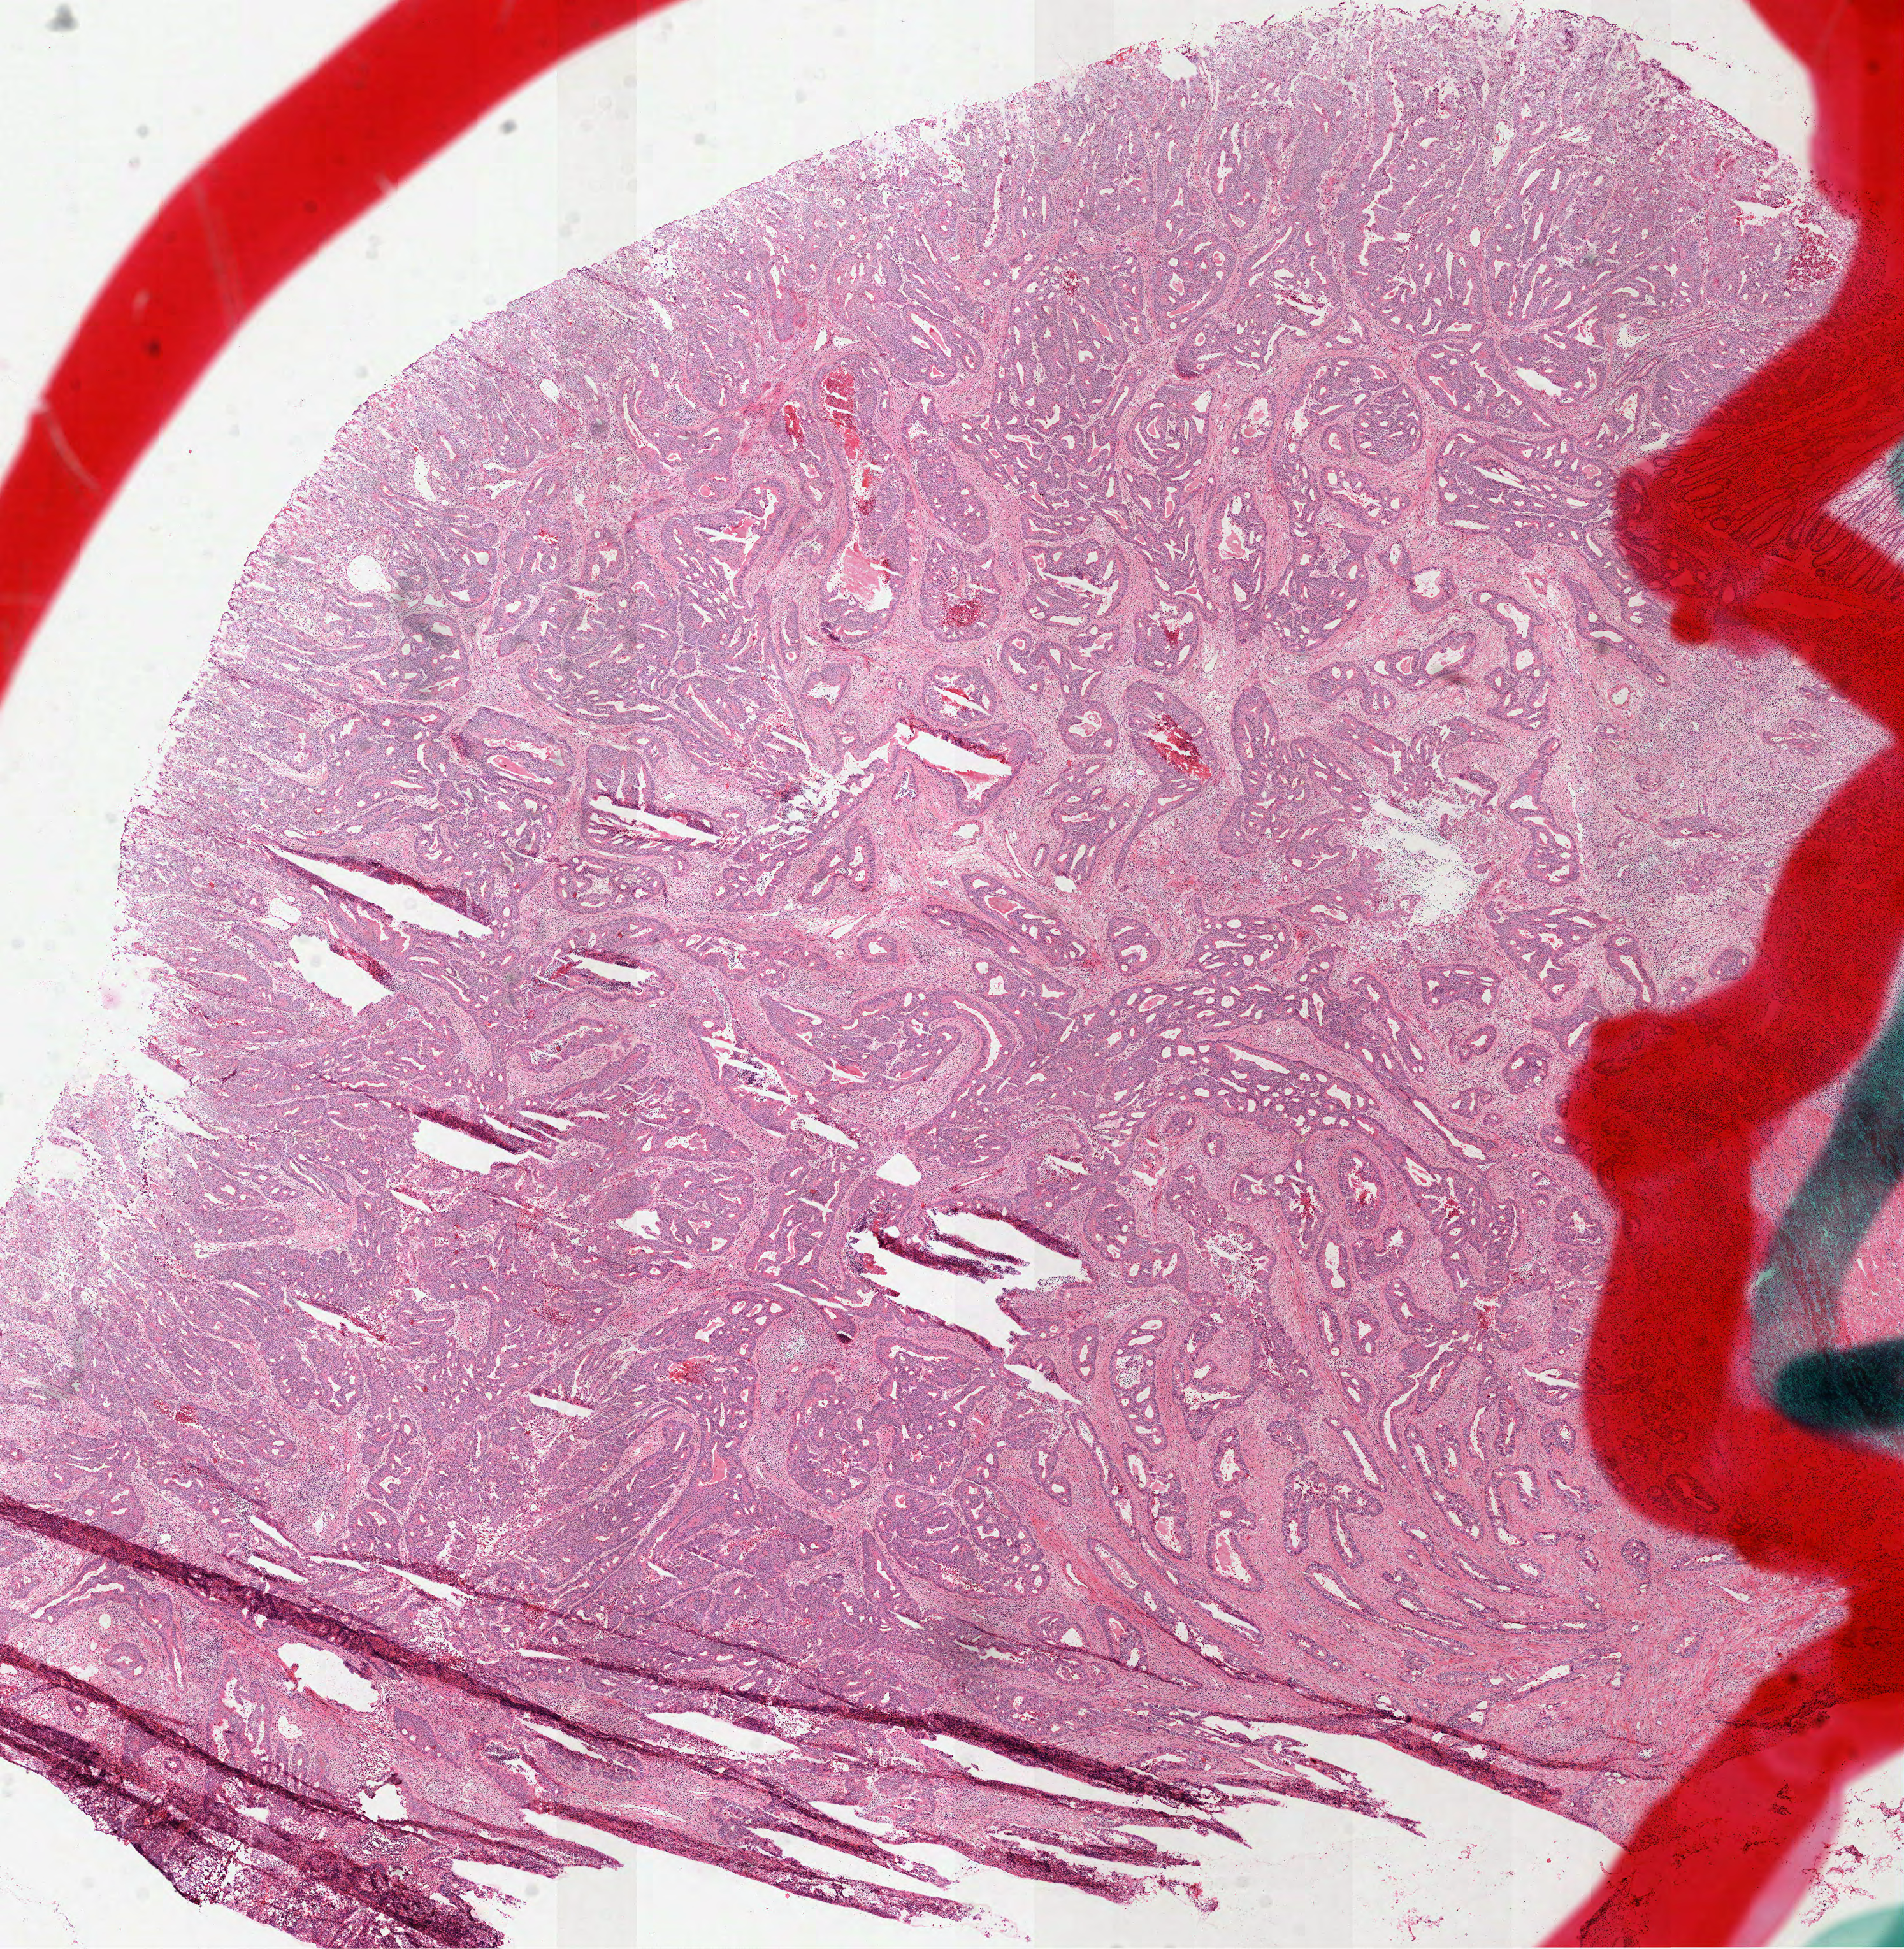
Hematoxylin and eosin (H&E) stained whole-slide image, whole scanned area (about 12.0 x 12.3 mm) shown as a low-resolution overview. Frozen section from the top of the tissue portion. Sample: primary tumour, rectum. Patient: female, age at initial diagnosis 64 years. Slide review estimates, as recorded: tumour cells 97%, tumour nuclei 80%, normal cells 0%, stromal cells 0%, necrosis 3%. Inflammatory infiltration, as recorded: lymphocyte infiltration 7%, monocyte infiltration 0%, neutrophil infiltration 2%.
AJCC pathologic stage: IIA (7th edition). Pathologic diagnosis: Adenocarcinoma, NOS (rectosigmoid junction).